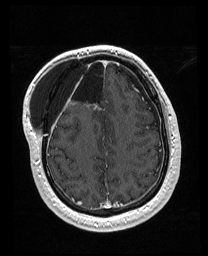
Brain MRI from a brain-tumour surgery series, one axial slice; position 56 of 176 along the scan axis; T1-weighted post-contrast; 1 mm slice thickness; 208 × 256 image matrix, field of view 208 × 256 mm. From the clinical record (not read from this slice): histopathology: Astrocytoma; WHO grade: 4; IDH mutation: yes.
Structures marked on this image (outlined manually by an expert reader):
- previous resection cavity: bounding box (x1, y1, x2, y2) in pixels: (68, 58, 101, 101)